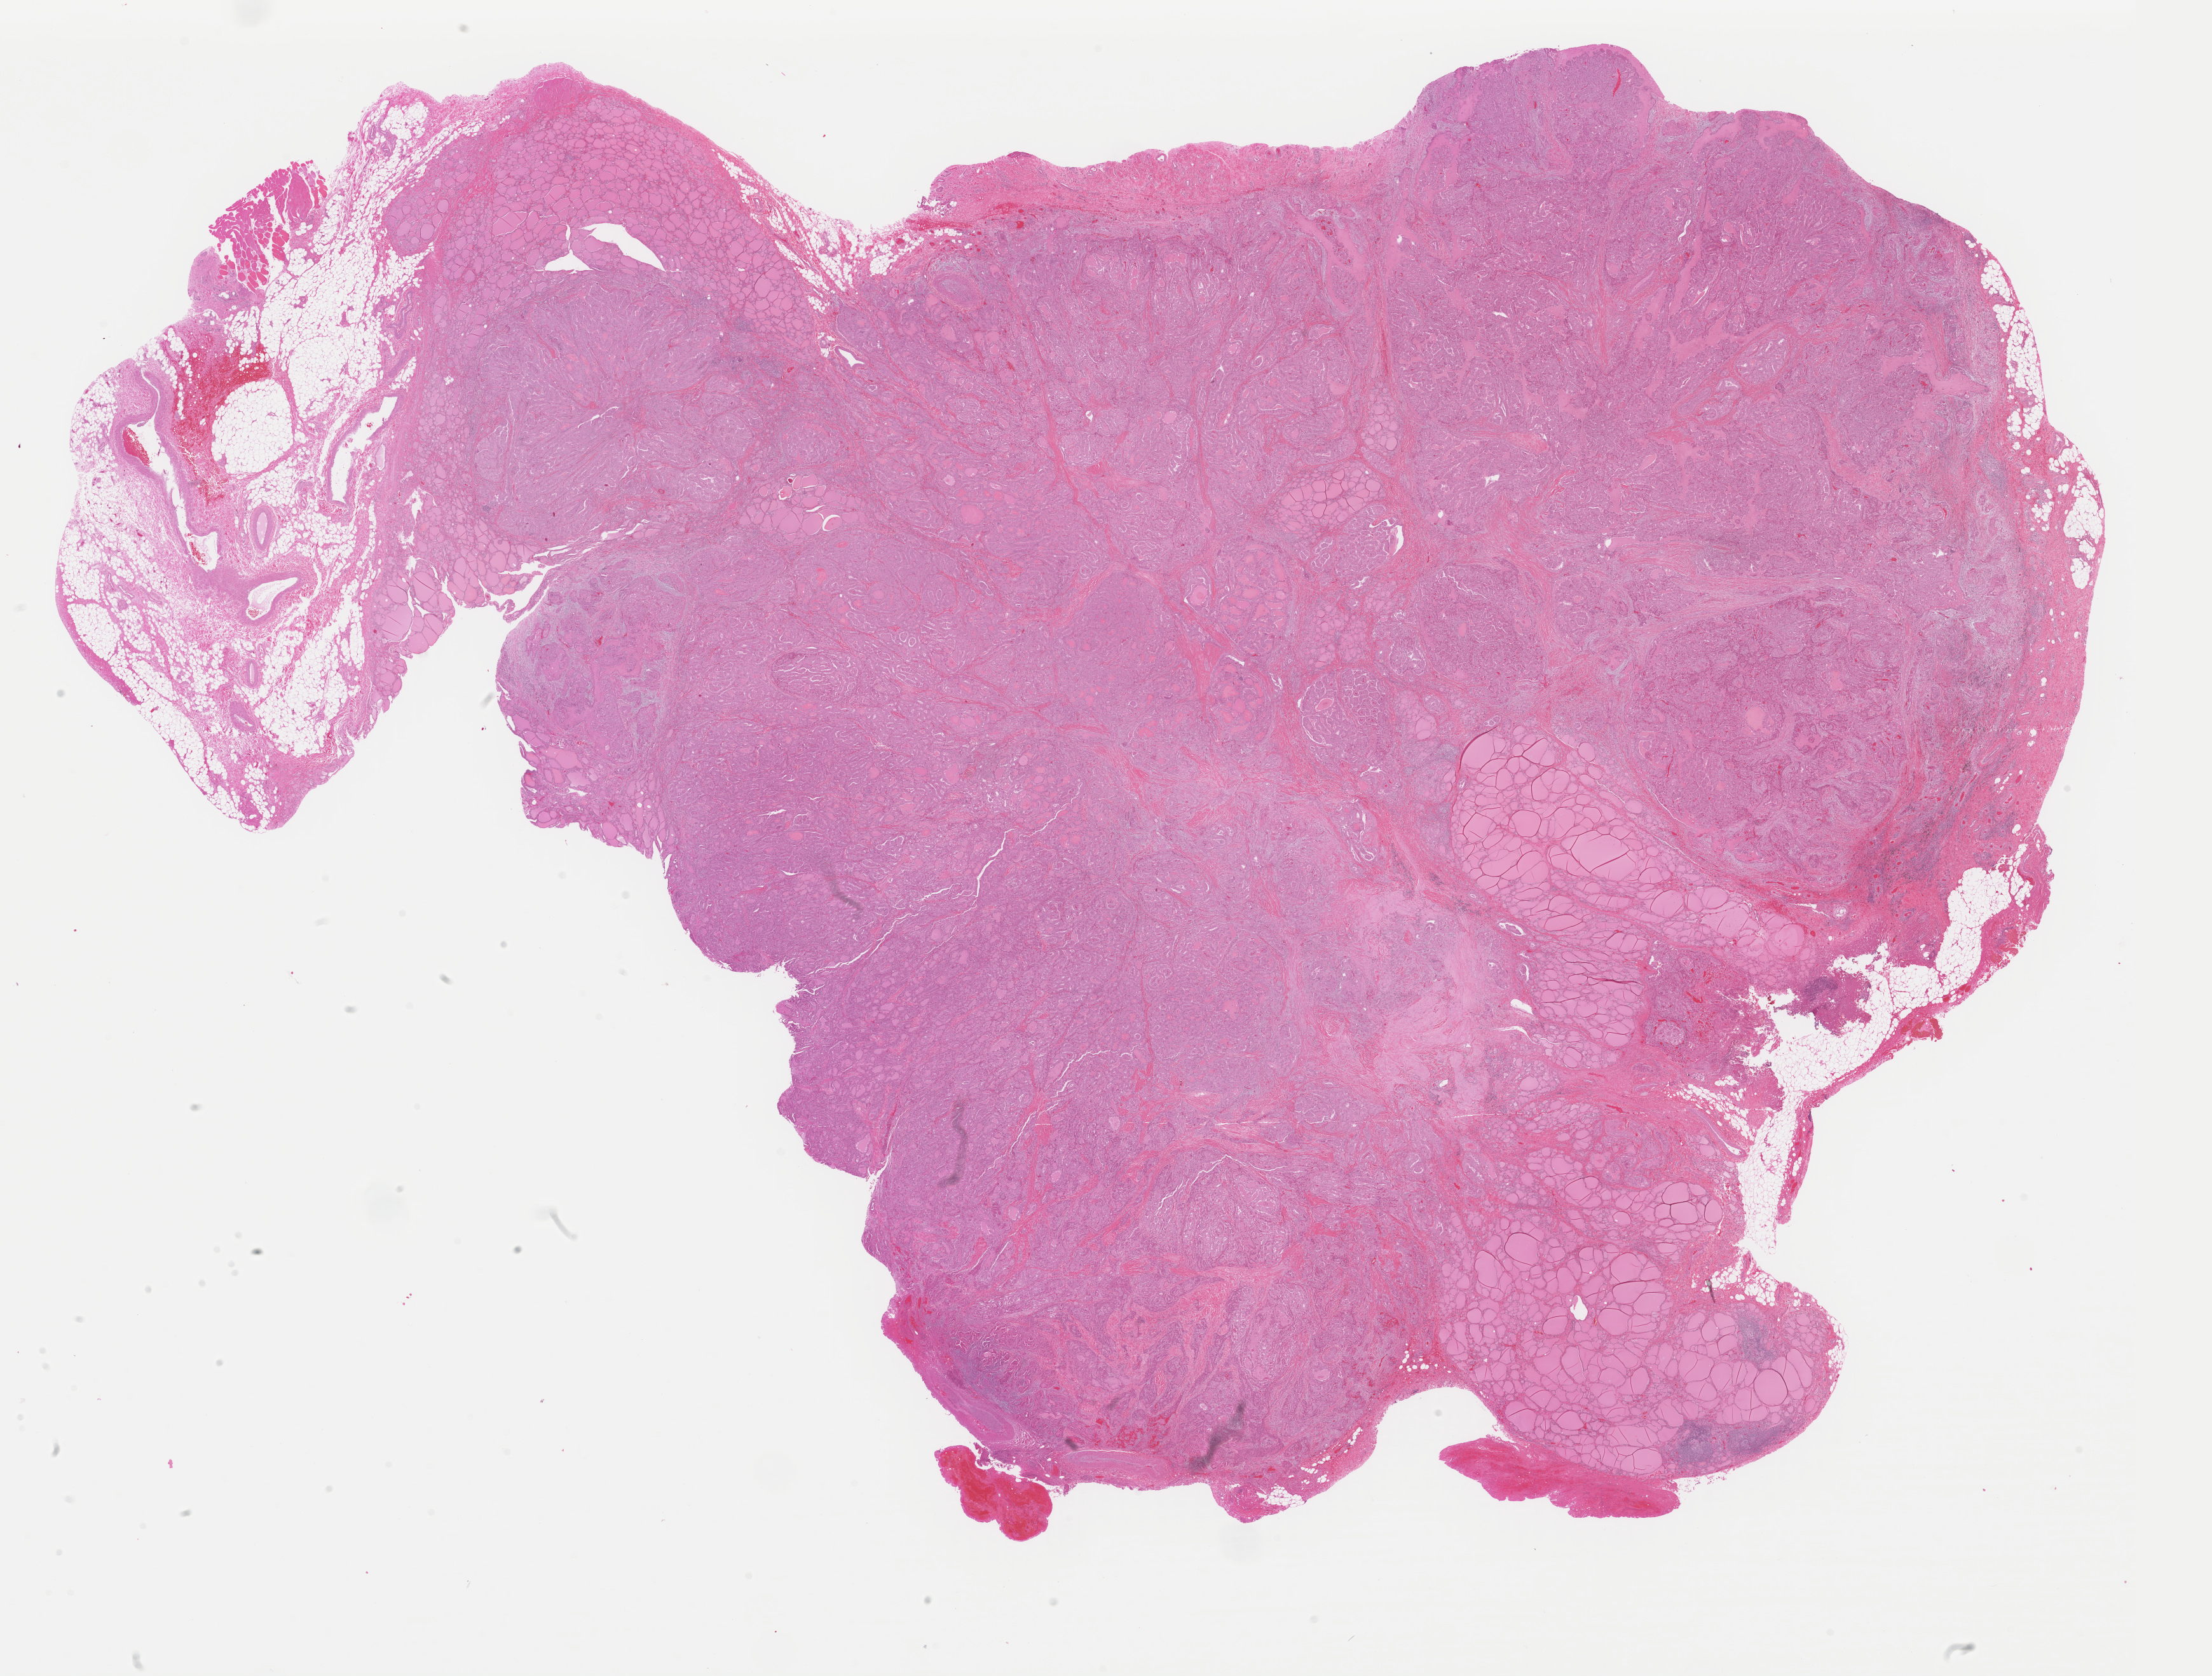
Whole-slide histology image, H&E-stained — shown as a low-resolution overview of the whole scanned area (about 27.5 x 20.8 mm, from a 40x scan). FFPE section. Primary tumour sample from the thyroid. Female patient; age at initial diagnosis 33 years.
* TNM: T3 N1 M0
* lymph nodes positive (case pathology): 13 of 43 examined
* AJCC pathologic stage: I (7th edition)
* histologic diagnosis: Papillary adenocarcinoma, NOS (thyroid gland)